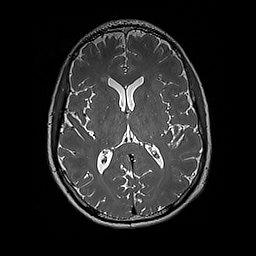
Brain MRI from a brain-tumour surgery series, one axial slice. Slice 93 of 192 in the series (ordered by position). 1 mm slice thickness. 256 × 256 image matrix, field of view 250 × 250 mm. Case-level facts recorded for this patient, not image findings: histopathology: Glioblastoma; WHO grade: 4; IDH mutation: no; tumour location: Left Insular.
Structures marked on this image (outlined manually by an expert reader):
- tumour: bounding box (x1, y1, x2, y2) in pixels: (158, 88, 163, 93)